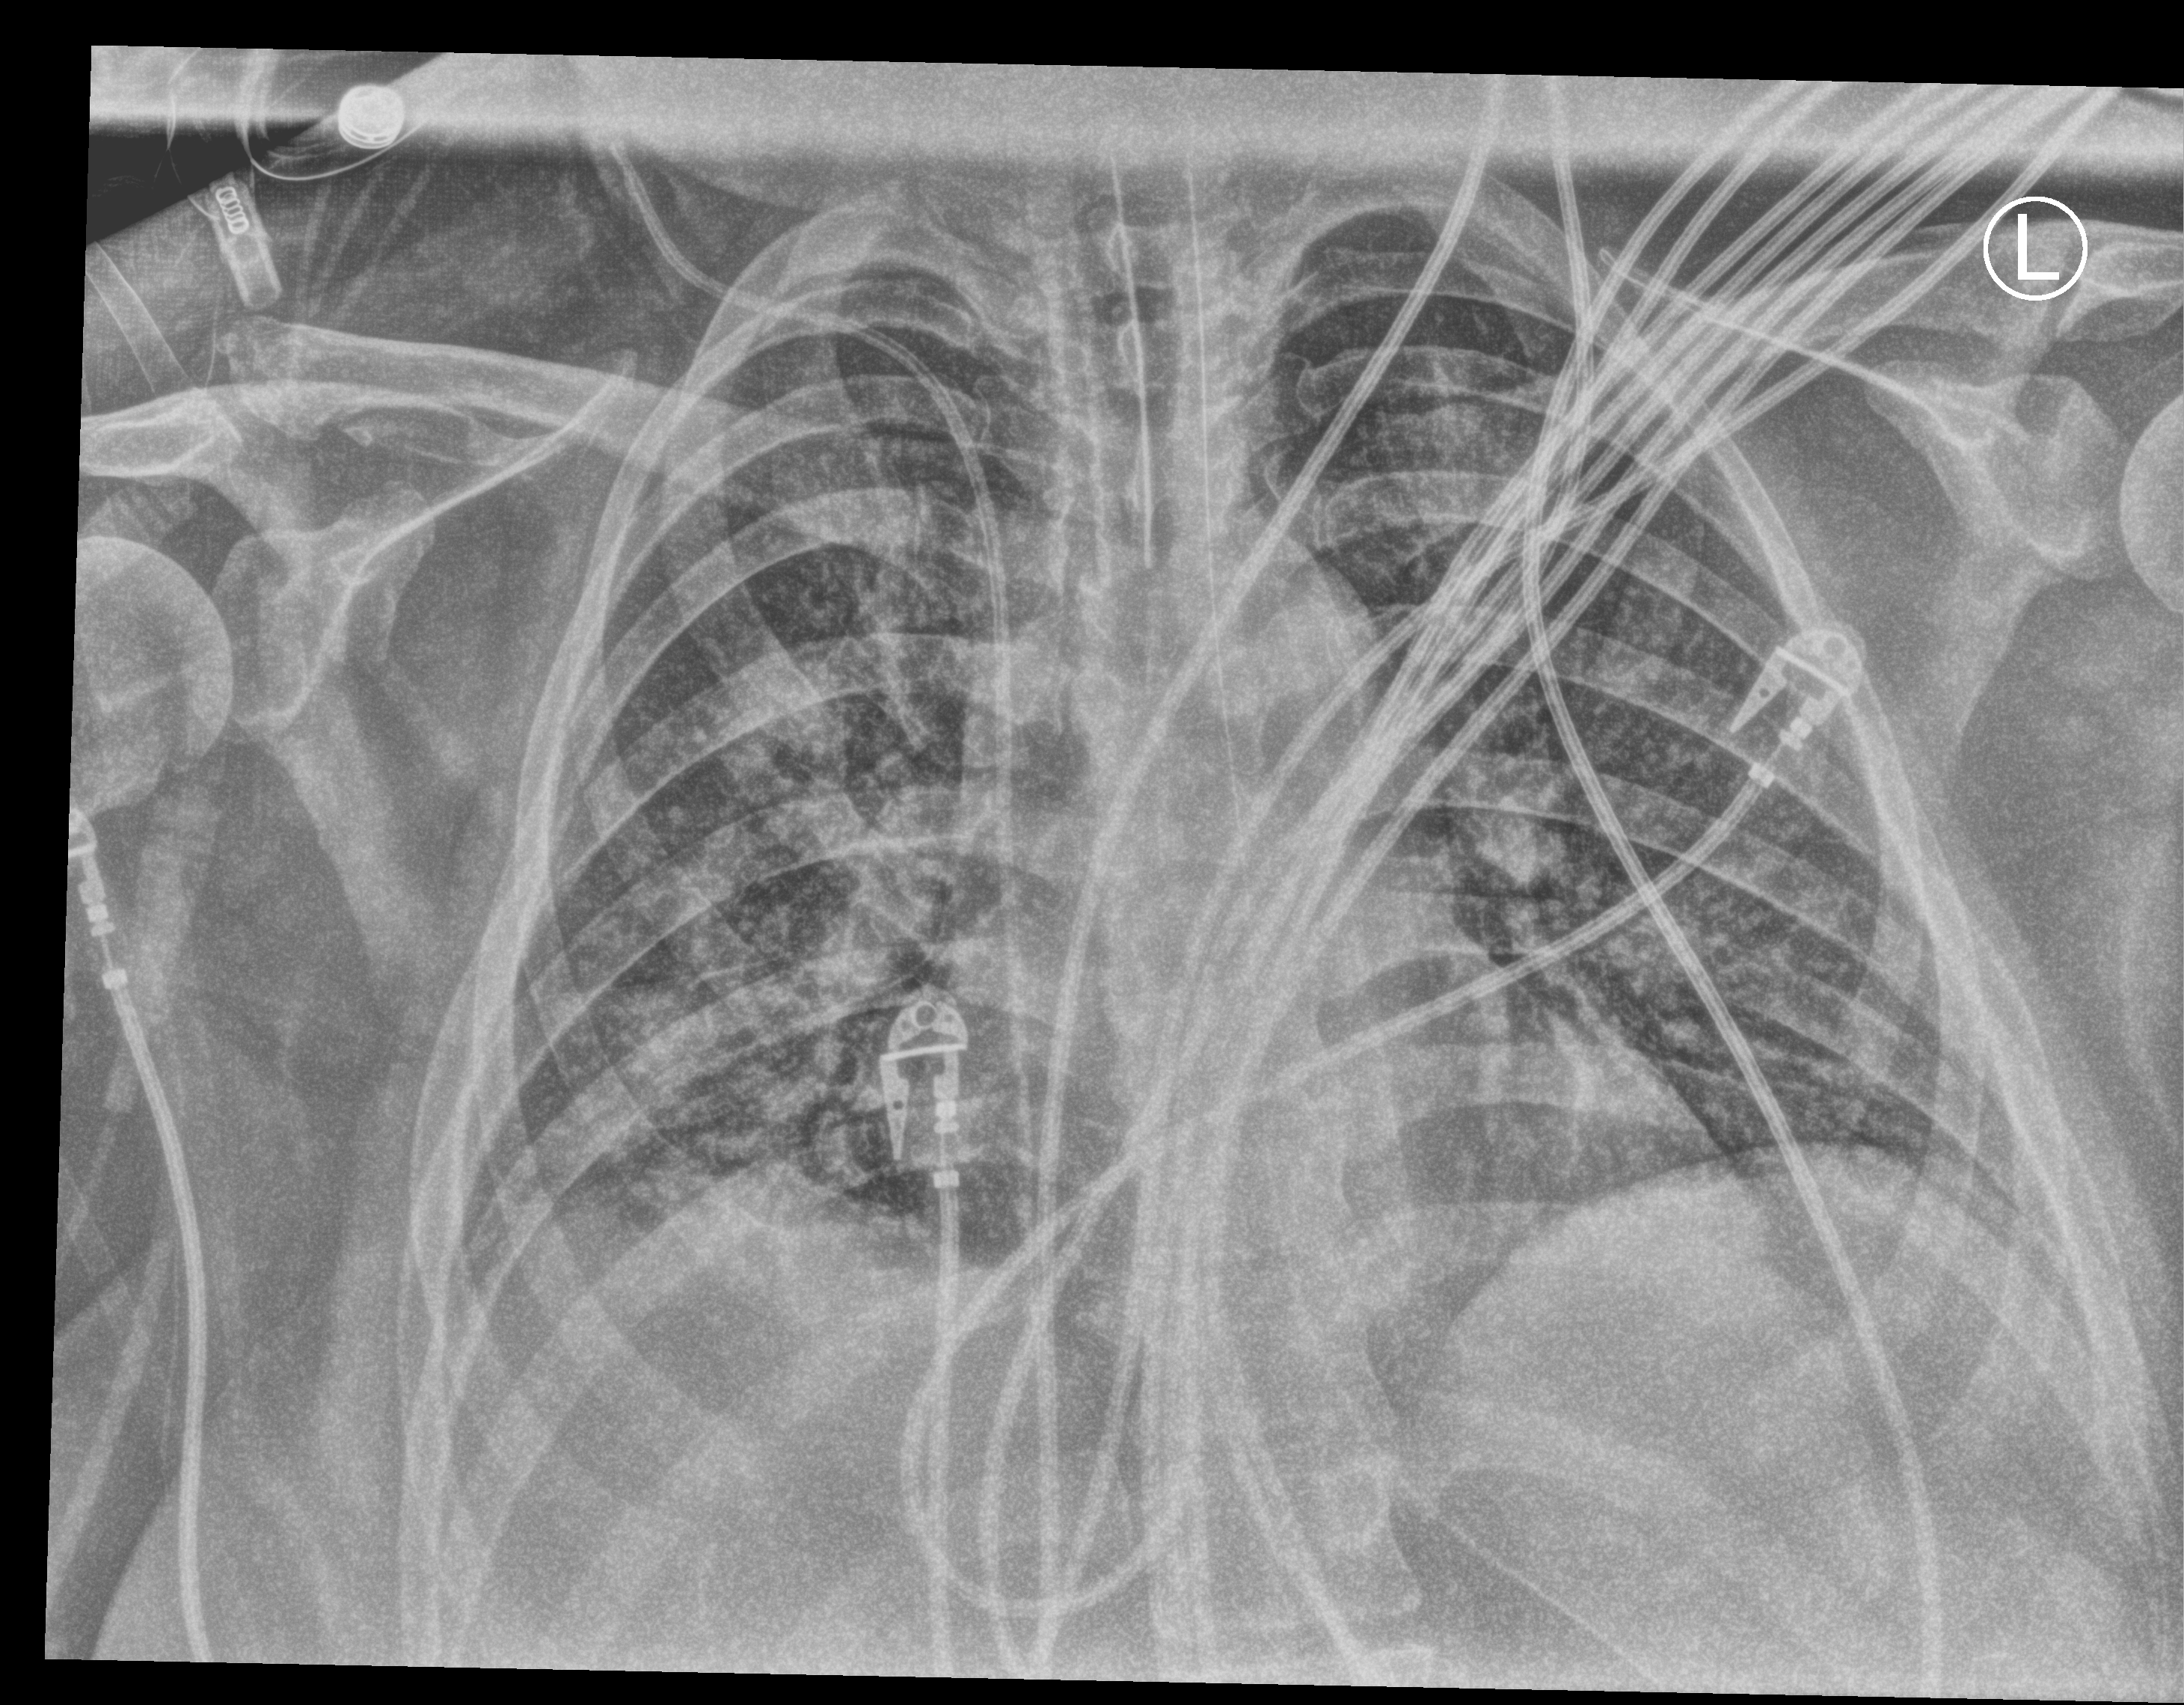
Bedside chest radiograph (computed radiography). Patient hospitalised with COVID-19; female, aged 18–59 years.
Admission-level facts for this patient (not findings on this image; timing relative to this image not recorded): mechanically ventilated during this hospital stay: yes; diabetes (admission record): no; admitted to intensive care during this hospital stay: yes.